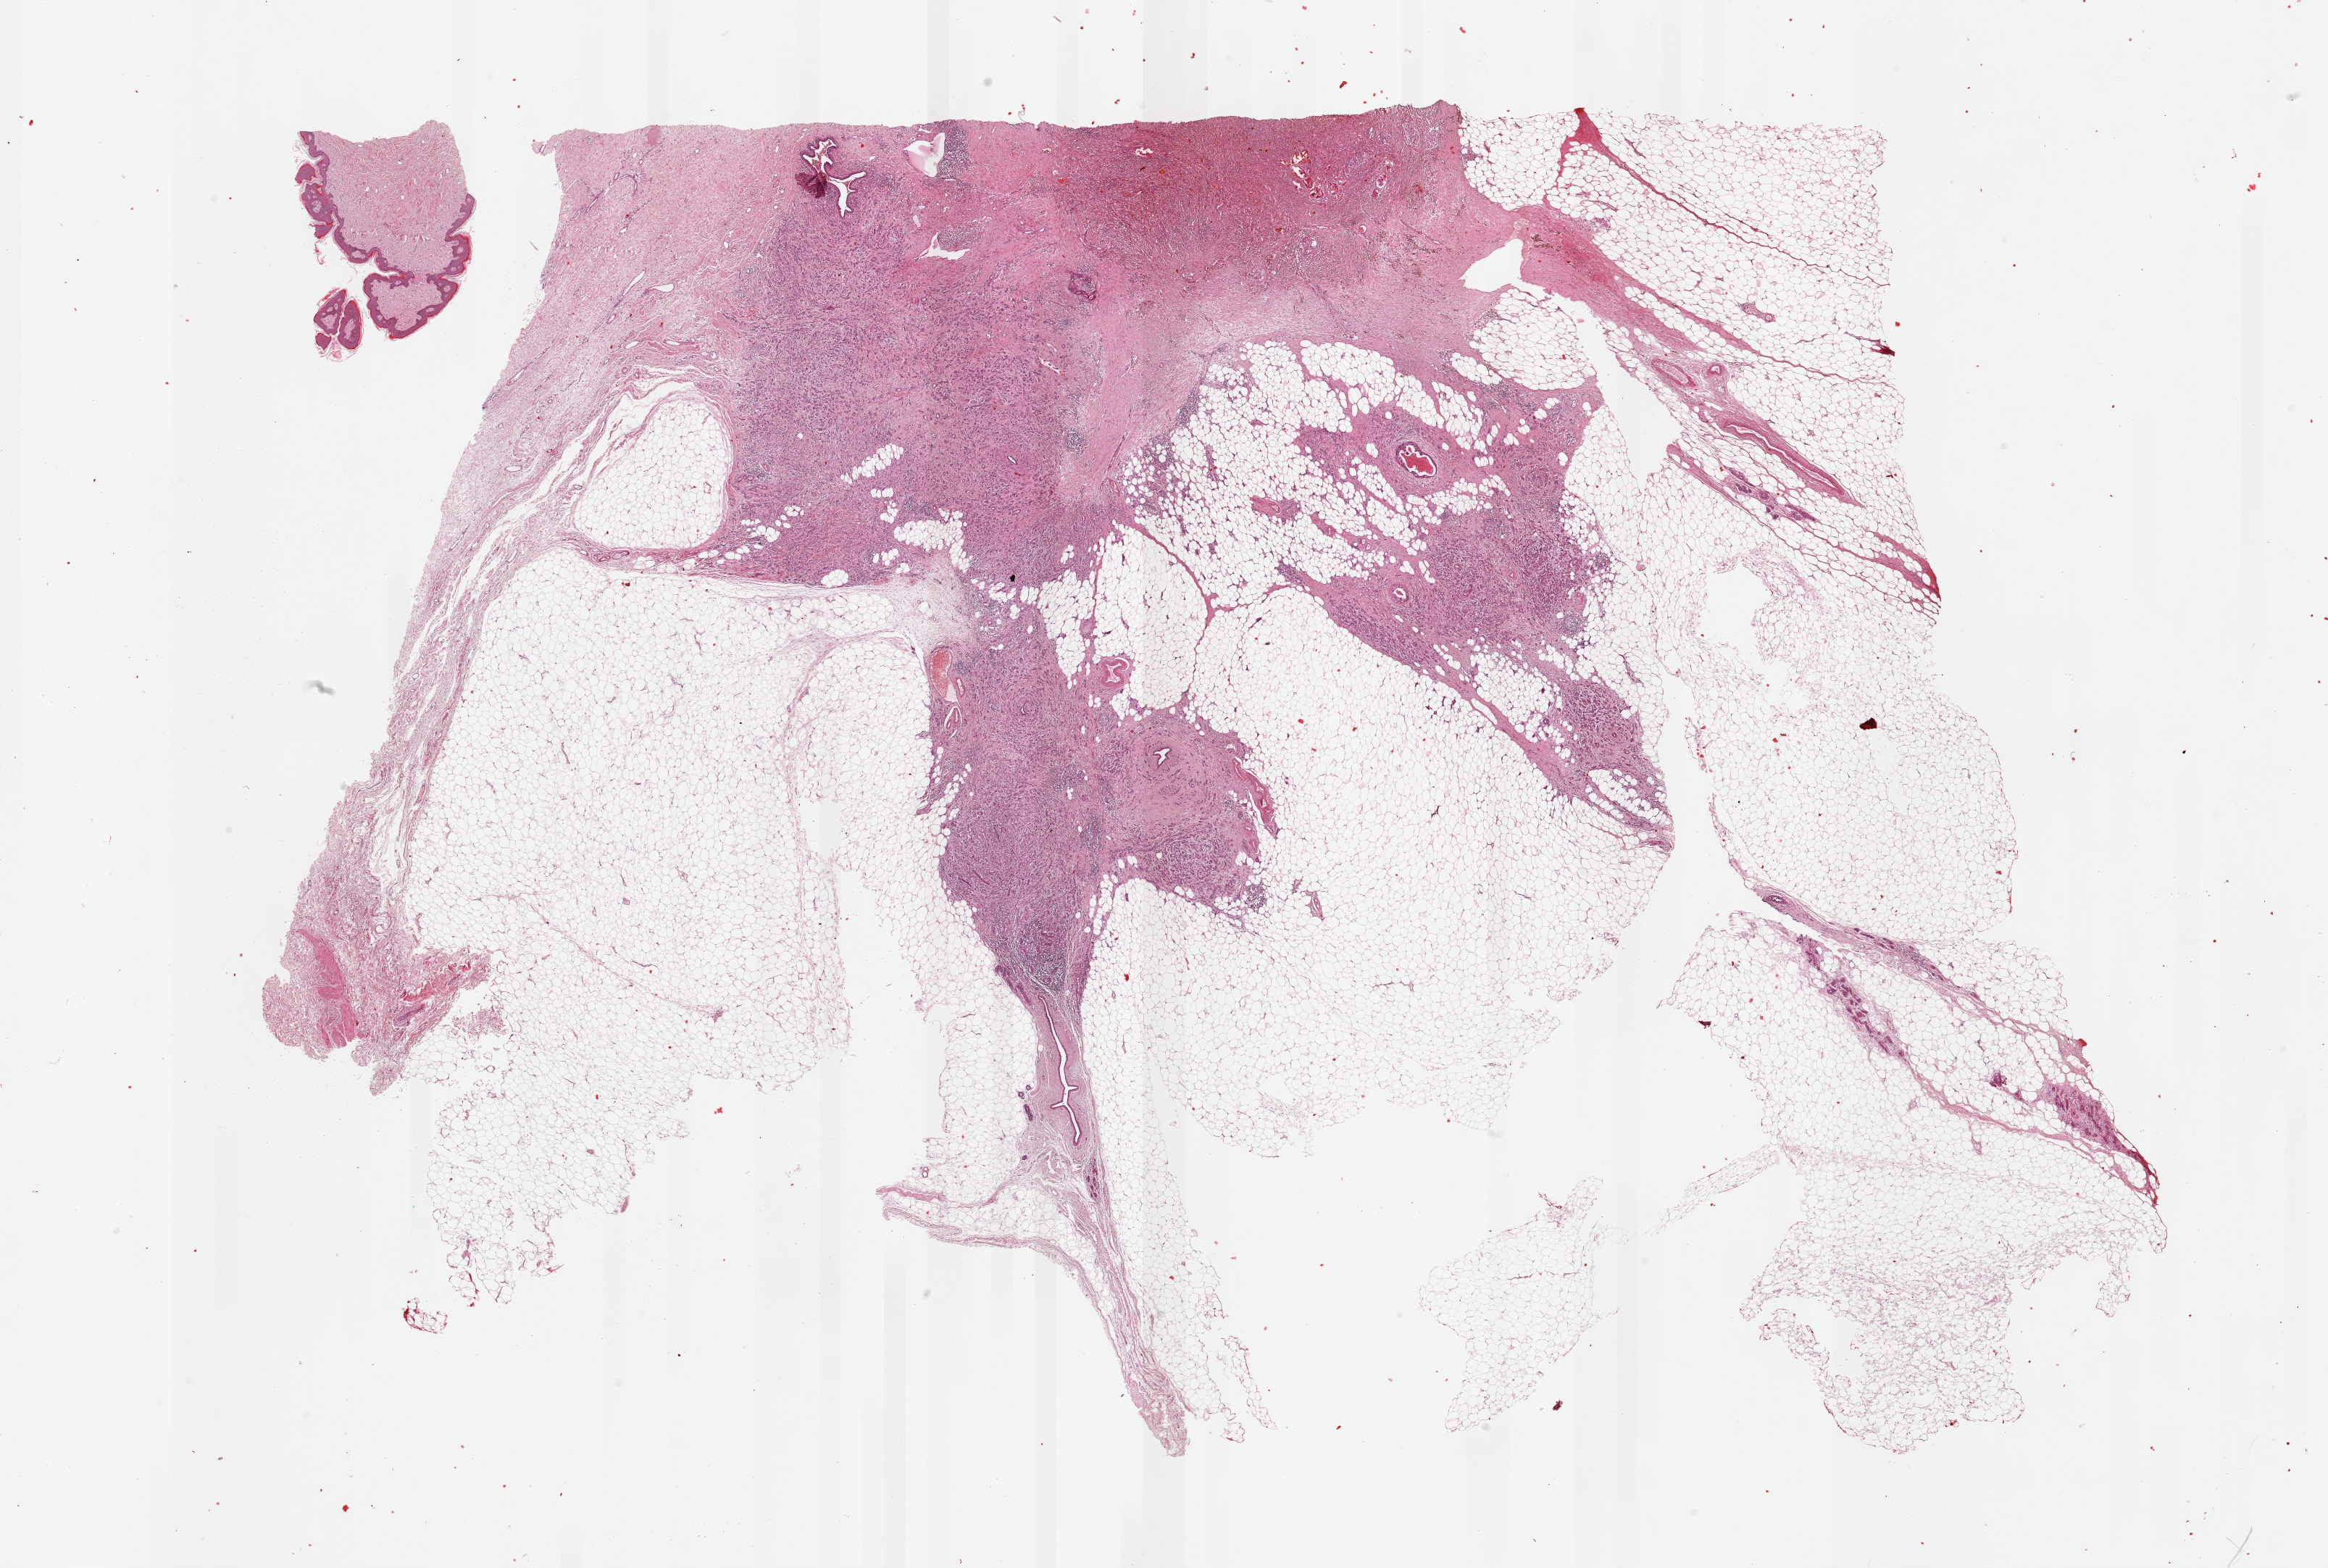
Whole-slide histology image, Hematoxylin and eosin (H&E) stained — whole scanned area (about 25.4 x 17.1 mm, from a 40x scan) shown as a low-resolution overview; FFPE section; breast, primary tumour sample. Patient: female, age at initial diagnosis 65 years.
Histologic diagnosis: Infiltrating duct carcinoma, NOS. AJCC pathologic stage: IIIA. Lymph nodes positive (case pathology): 9 of 15 examined. Laterality: left.